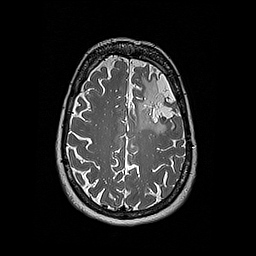
Brain MRI from a brain-tumour surgery series, one axial slice. Slice 131 of 192 in the series (ordered by position). 256 × 256 image matrix. From the clinical record (not read from this slice): histopathology: Oligodendroglioma; WHO grade: 2; IDH mutation: yes.
Annotated regions visible in this slice (manually delineated by an expert):
- tumour: box from (x=133, y=79) to (x=157, y=131) px